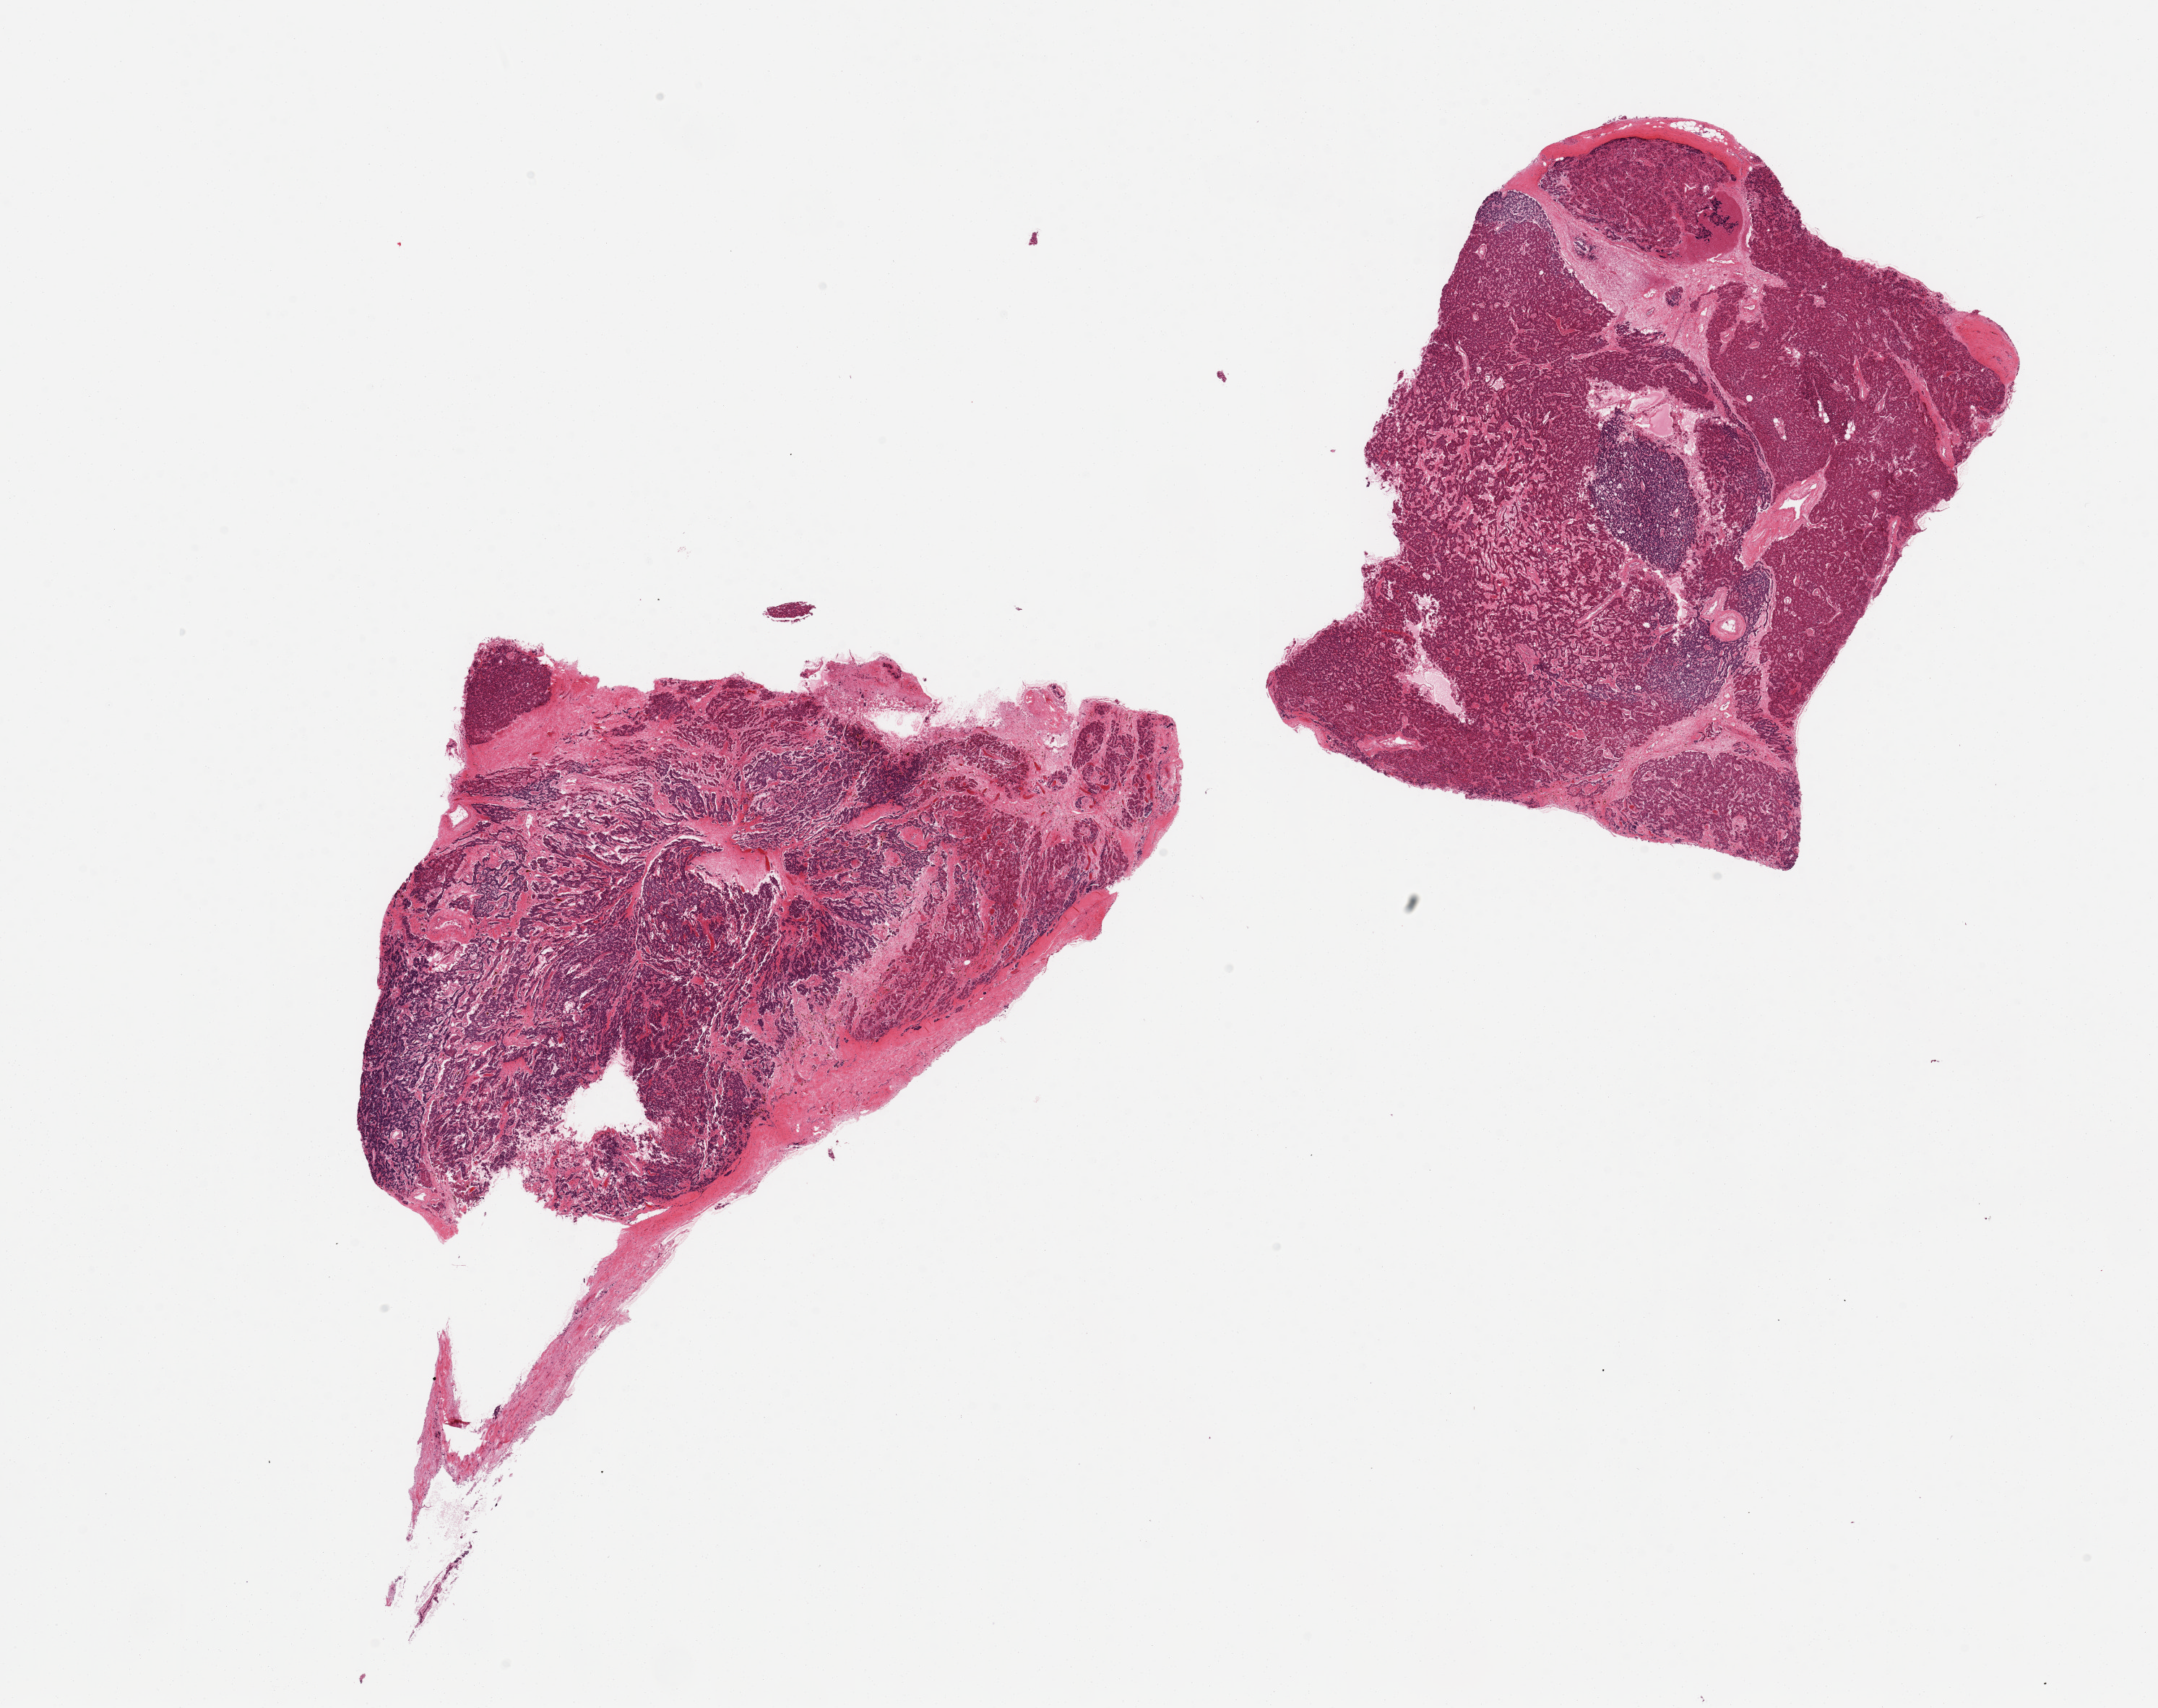
Digitized H&E-stained section, brightfield, whole scanned area (about 23.6 x 18.7 mm, slide scanned at 20x) shown as a low-resolution overview. PAXgene-fixed, paraffin-embedded tissue. Target tissue: thyroid. Donor tissue sample. Donor: male.
- reviewer comment on this tissue sample: 2 pieces, abnormal, infiltrating neoplasm, oncocytic features, effaaces entire specimen